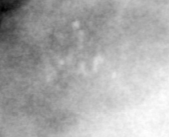
Region of interest cut from a scanned film mammogram (one marked finding); left breast; MLO view; BI-RADS breast density category 4 (scale 1–4).
Calcifications, morphology pleomorphic, distribution clustered; BI-RADS assessment category 4; subtlety rating 2 on a 1 (subtle) to 5 (obvious) scale; pathology result (as recorded, not read from the image): malignant.